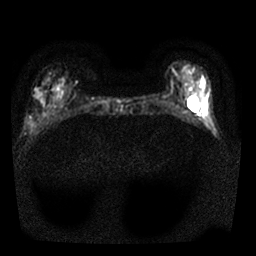
Breast MRI, one axial slice. Diffusion-weighted series; image 2 of 4 stored at this slice position (different b-values; order by instance number). 1.5 T. 256 × 256 image matrix, field of view 310 × 310 mm. Female patient.
Outlined on this slice (expert manual segmentation):
- tumour on diffusion-weighted imaging: bounding box [x1, y1, x2, y2] px = [34, 89, 43, 98]